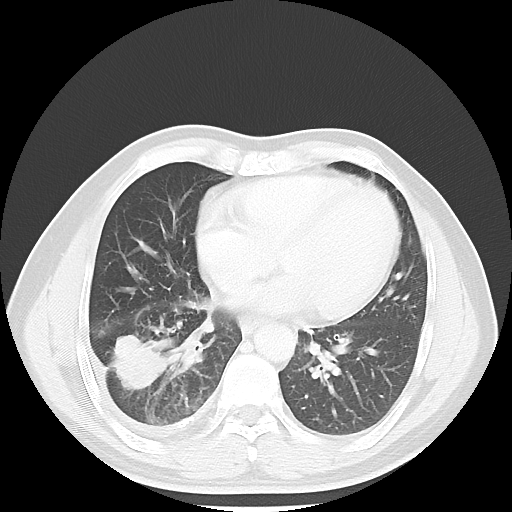
Chest CT, one axial slice; slice 22 of 56 in the series (ordered by position); reconstruction kernel LUNG; lung window (W 1500 / L -600 HU); 5 mm slice thickness; 512 × 512 image matrix. Male patient, age 56 years. From the clinical record (not read from this slice): clinical TNM (as recorded): T2 N3 M1.
Outlined on this slice (rectangle marked by the reading radiologist):
- lung tumour (recorded histology: adenocarcinoma): bounding box <111,327,171,399> (left, top, right, bottom; pixels)